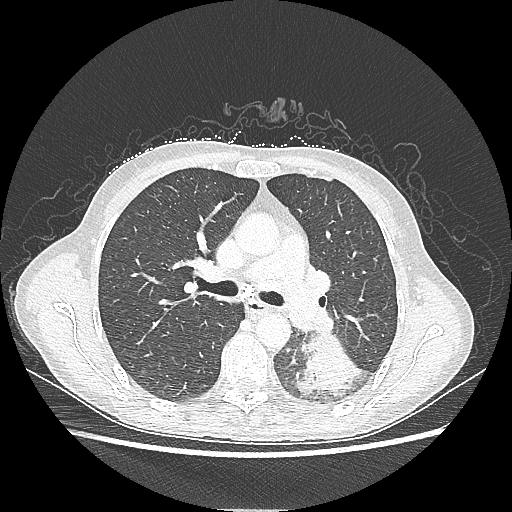
Chest CT, one axial slice; position 135 of 220 along the scan axis; 80 kVp; lung window (W 1500 / L -600 HU); 1.25 mm slice thickness; 512 × 512 image matrix, field of view 360 × 360 mm. Female patient, age 53 years. From the clinical record (not read from this slice): clinical TNM (as recorded): T3 N0 M0.
Annotated regions visible in this slice (rectangle marked by the reading radiologist):
- lung tumour (recorded histology: adenocarcinoma): bounding box [x1, y1, x2, y2] px = [294, 332, 363, 399]